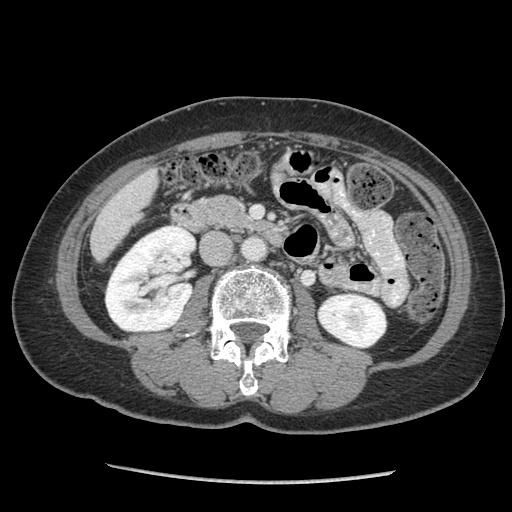
Contrast-enhanced abdominal CT (liver protocol), one axial slice; position 20 of 105 along the scan axis; reconstruction kernel STANDARD; 140 kVp; soft-tissue window (W 400 / L 40 HU); 2.5 mm slice thickness; 512 × 512 image matrix. From the clinical record (not read from this slice): diagnosis: hepatocellular carcinoma (patient treated with transarterial chemoembolisation; whether this scan precedes or follows treatment is not stated here); TNM stage (as recorded): Stage-I; Child-Pugh class: A; tumour differentiation: moderately differentiated.
Outlined on this slice (semi-automatic segmentation, software-assisted and operator-edited):
- liver parenchyma outside the tumour (the mass and vessels are separate outlines, so this box may not span the whole liver): box from (x=90, y=168) to (x=158, y=260) px